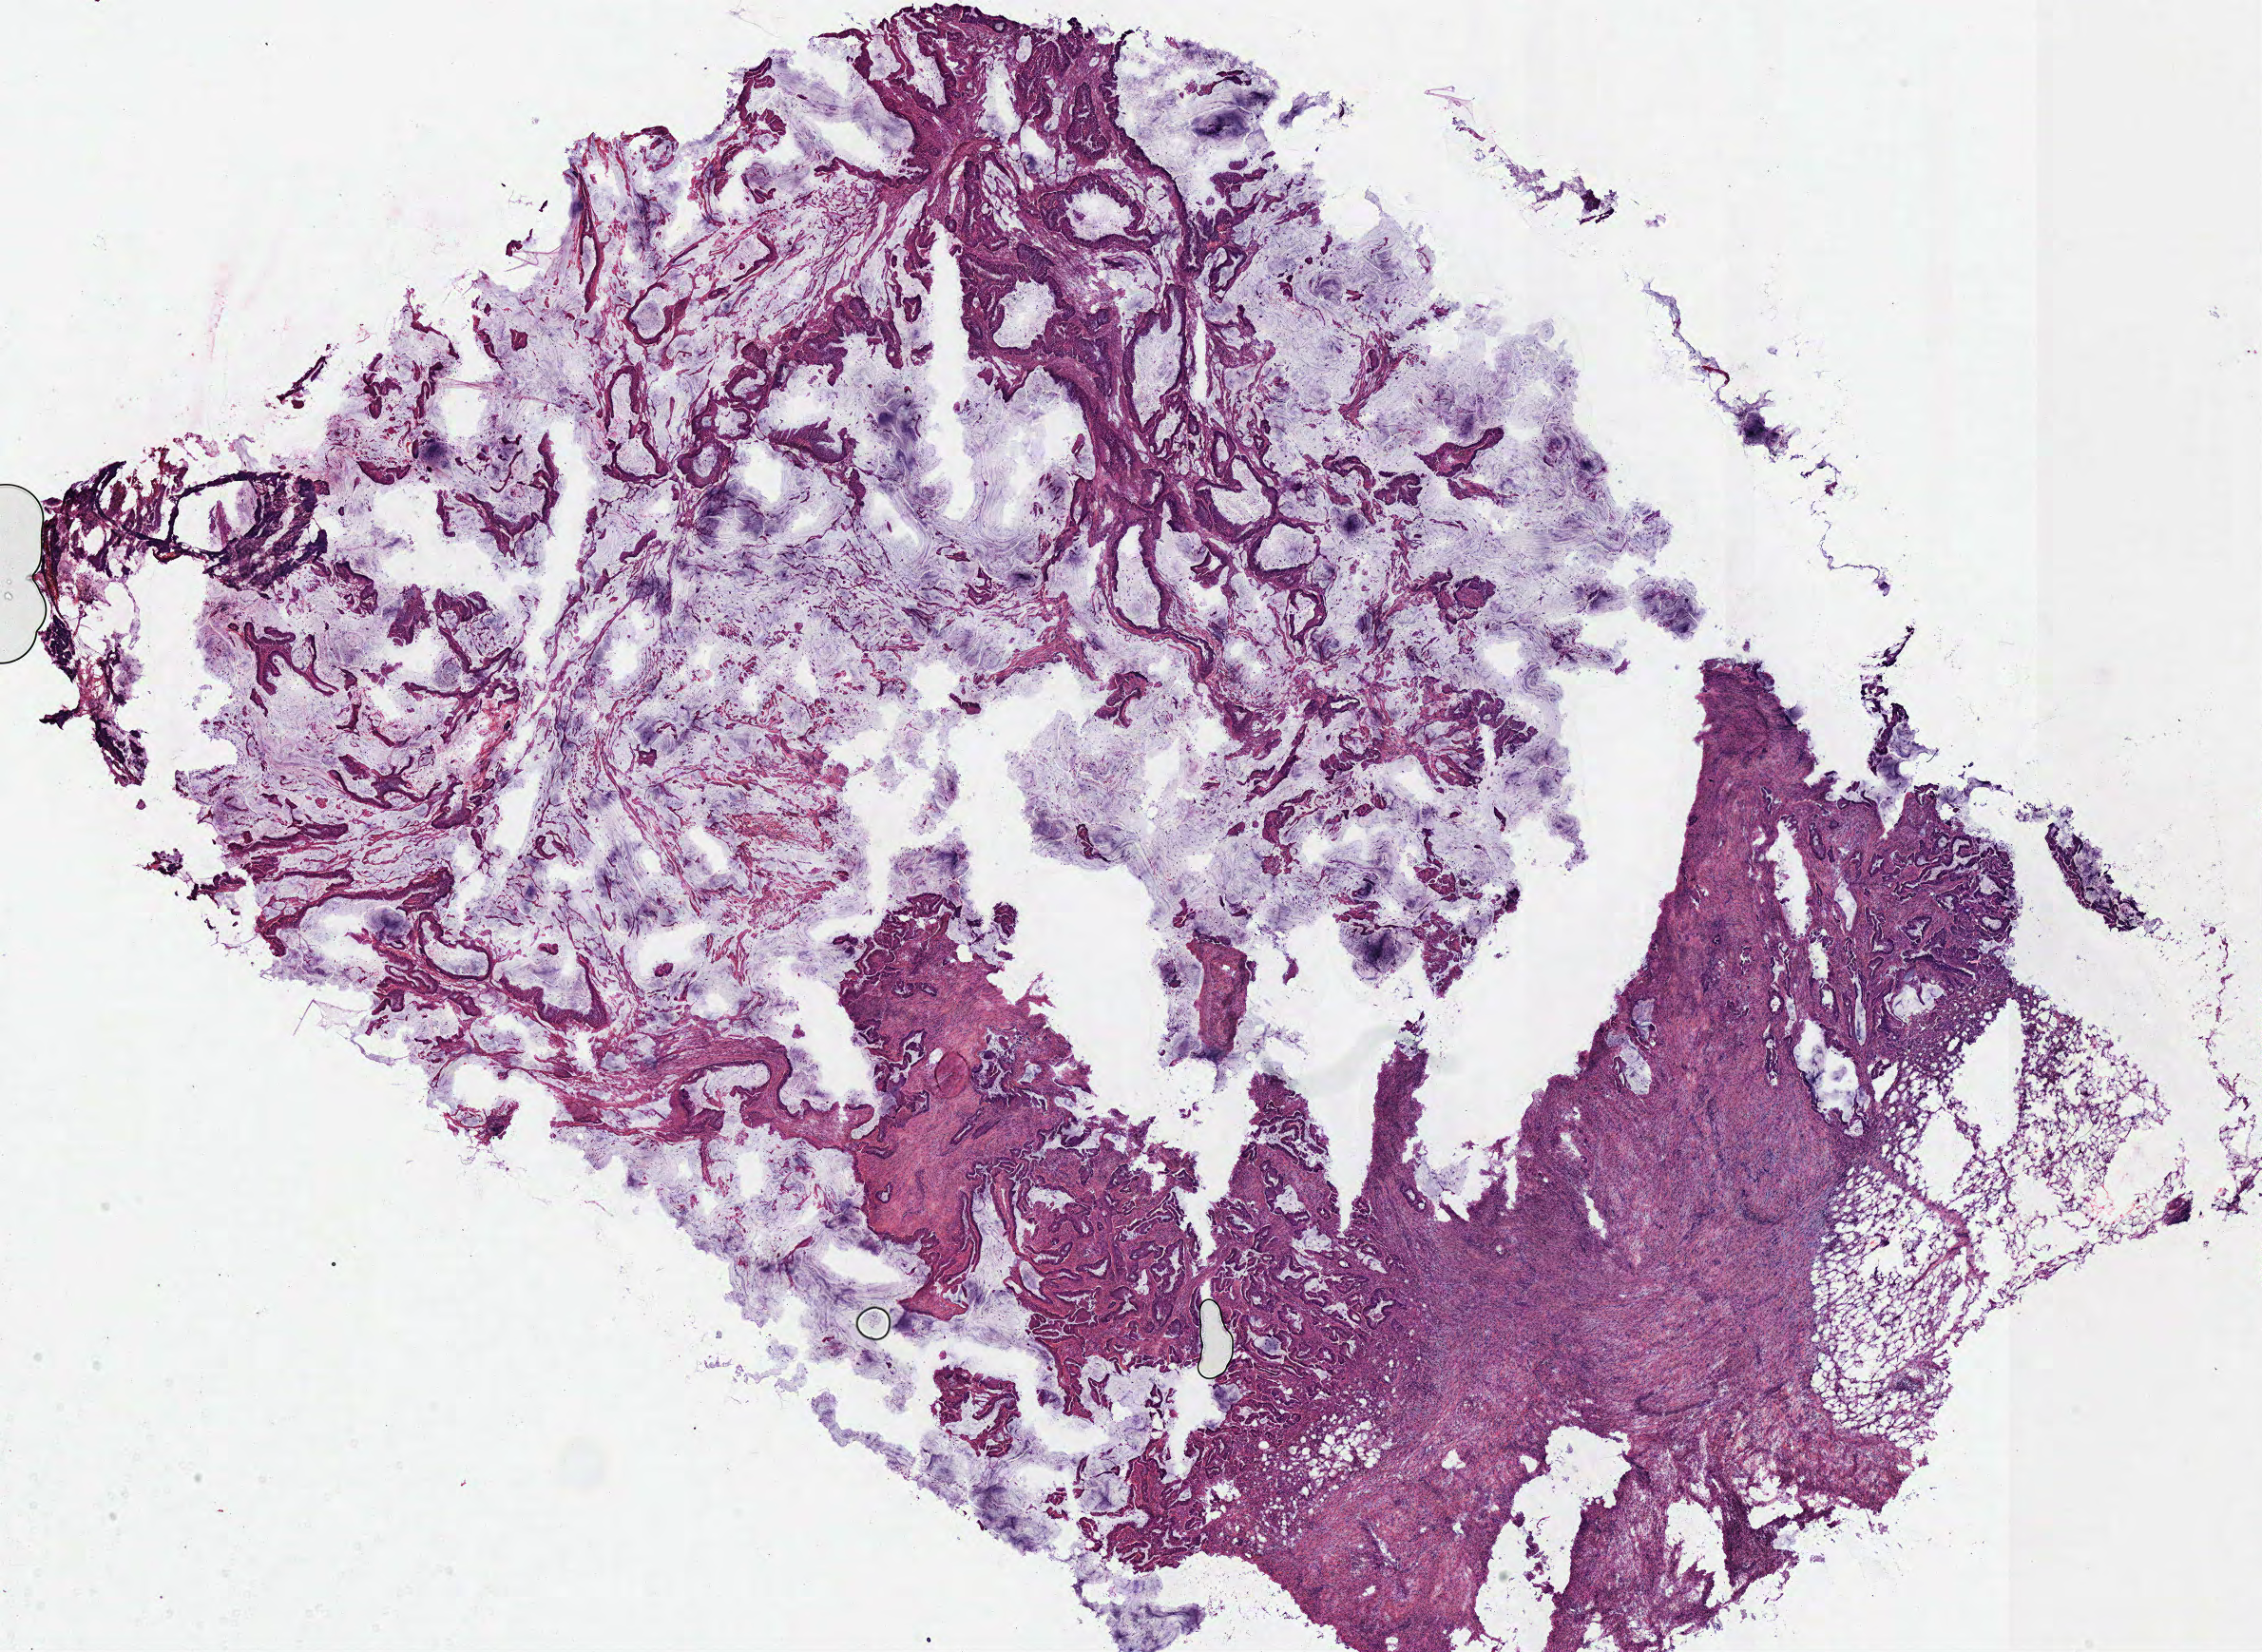
Digitized H&E-stained tissue section (whole slide) — low-resolution overview of the scanned area, about 18.8 x 13.7 mm; frozen section from the bottom of the tissue portion; sample: primary tumour, colon. Female, age 70 years at initial diagnosis. Composition of this section per pathologist review: tumour cells 70%, tumour nuclei 70%, normal cells 0%, stromal cells 30%, necrosis 0%.
• histologic diagnosis: Adenocarcinoma, NOS (sigmoid colon)
• AJCC pathologic stage: IIA (7th edition)